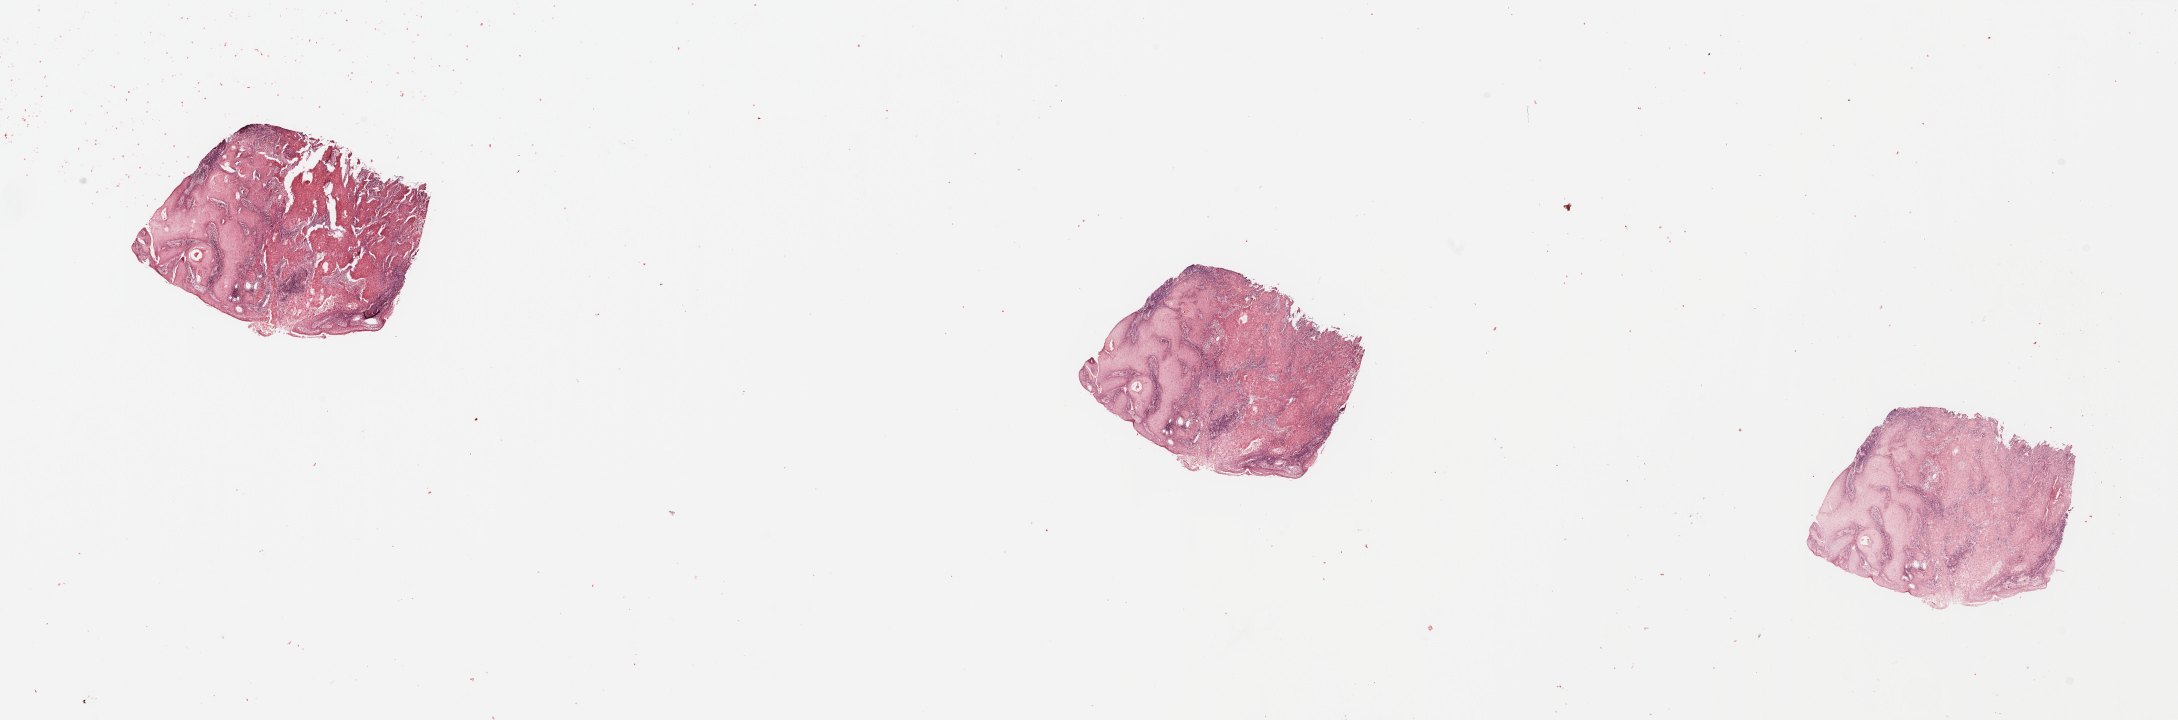
Digitized H&E tissue section (whole slide) — low-resolution overview of the scanned area, about 34.5 x 11.4 mm, tumour tissue sample, sampled site: tongue. Female, 55 y/o. Histologic grade: G2 (moderately differentiated). Composition of this section per pathologist review: tumour nuclei 85%, necrosis 3%.
AJCC pathologic stage: IVA. Primary tumour site (as recorded): oral cavity. Diagnosis: Squamous cell carcinoma, NOS (tongue, NOS).